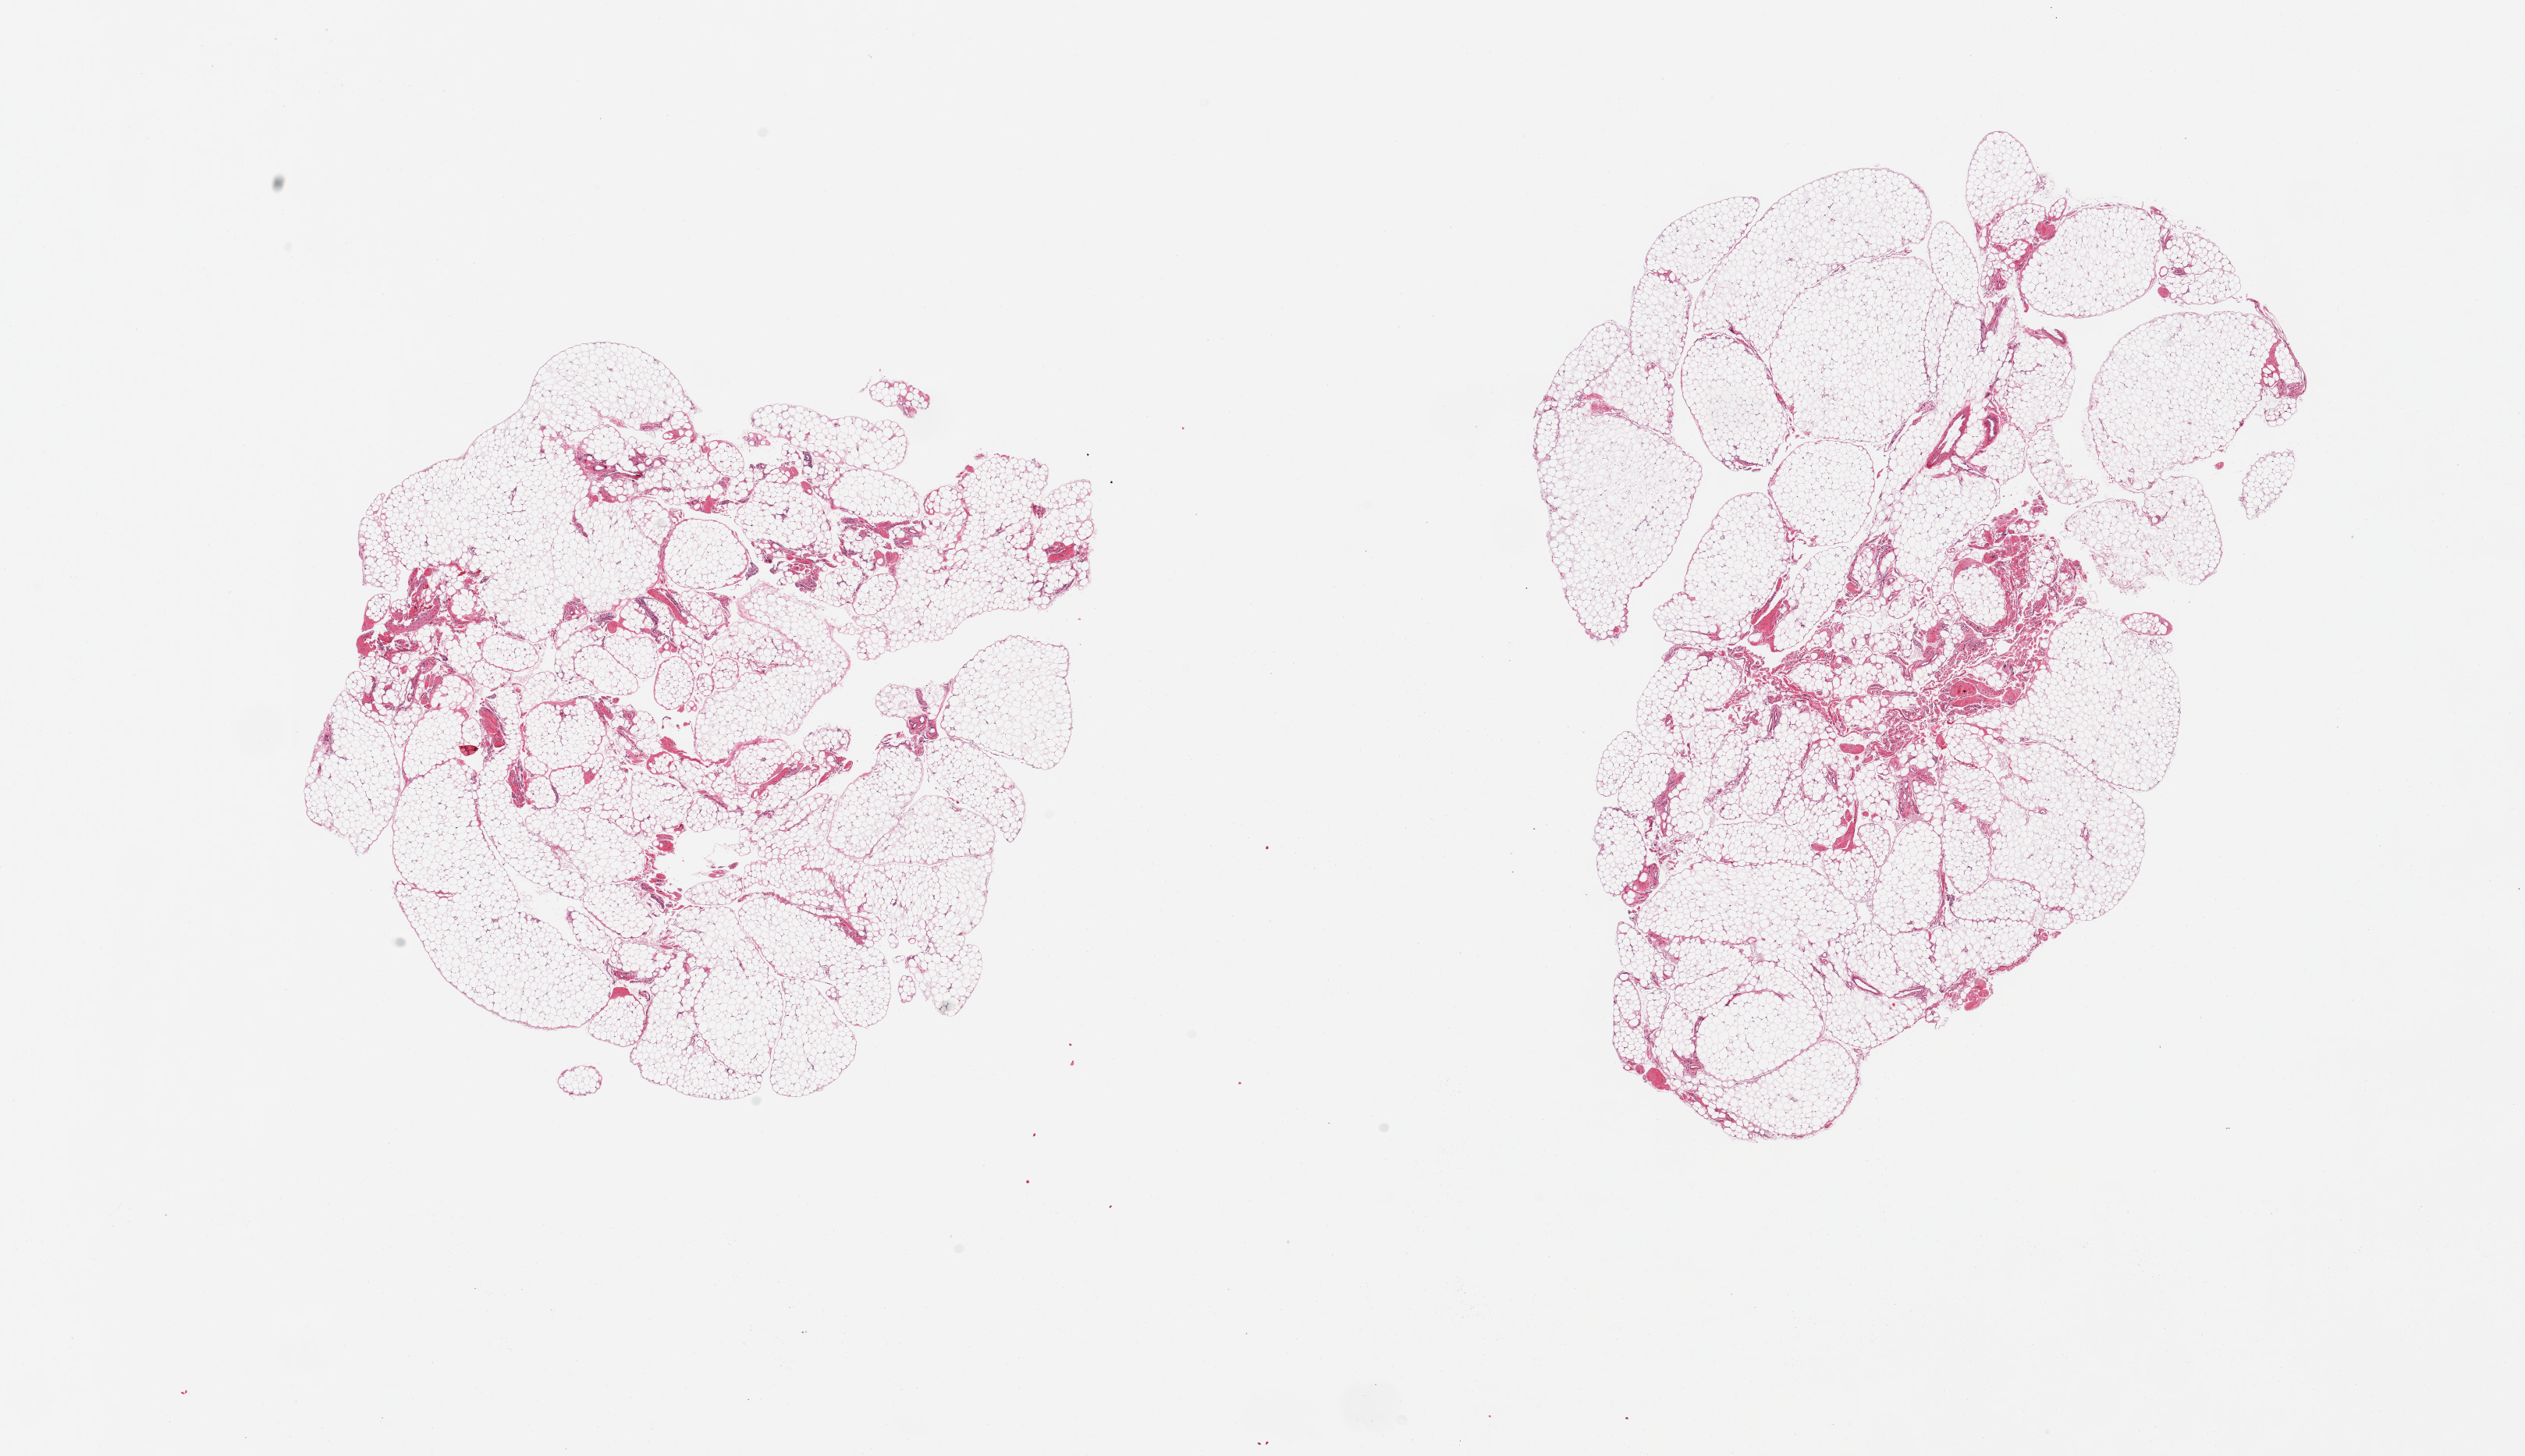
Haematoxylin and eosin whole-slide image, whole scanned area (about 25.6 x 14.8 mm, acquisition: 20x scan) shown as a low-resolution overview, PAXgene-fixed paraffin-embedded (PFPE) section, sampled site (target tissue): omentum, donor tissue sample. Donor: male.
* pathologist's review note for this sample: 2 pieces; lobulated mature fat with small fibrous component